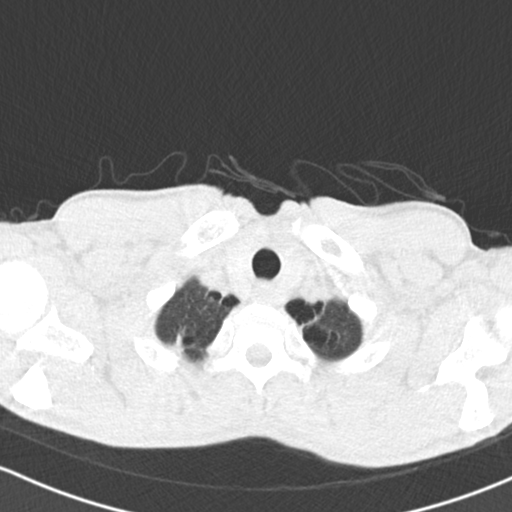
Low-dose screening chest CT, one axial slice. Slice 131 of 150 in the series (ordered by position). Reconstruction kernel B30f. 120 kVp. Lung window (W 1500 / L -600 HU). 2 mm slice thickness. 512 × 512 image matrix, field of view 312 × 312 mm.
Outlined on this slice (expert manual segmentation):
- lesion 1 (tumor, upper lobe of right lung): box from (x=172, y=334) to (x=183, y=348) px